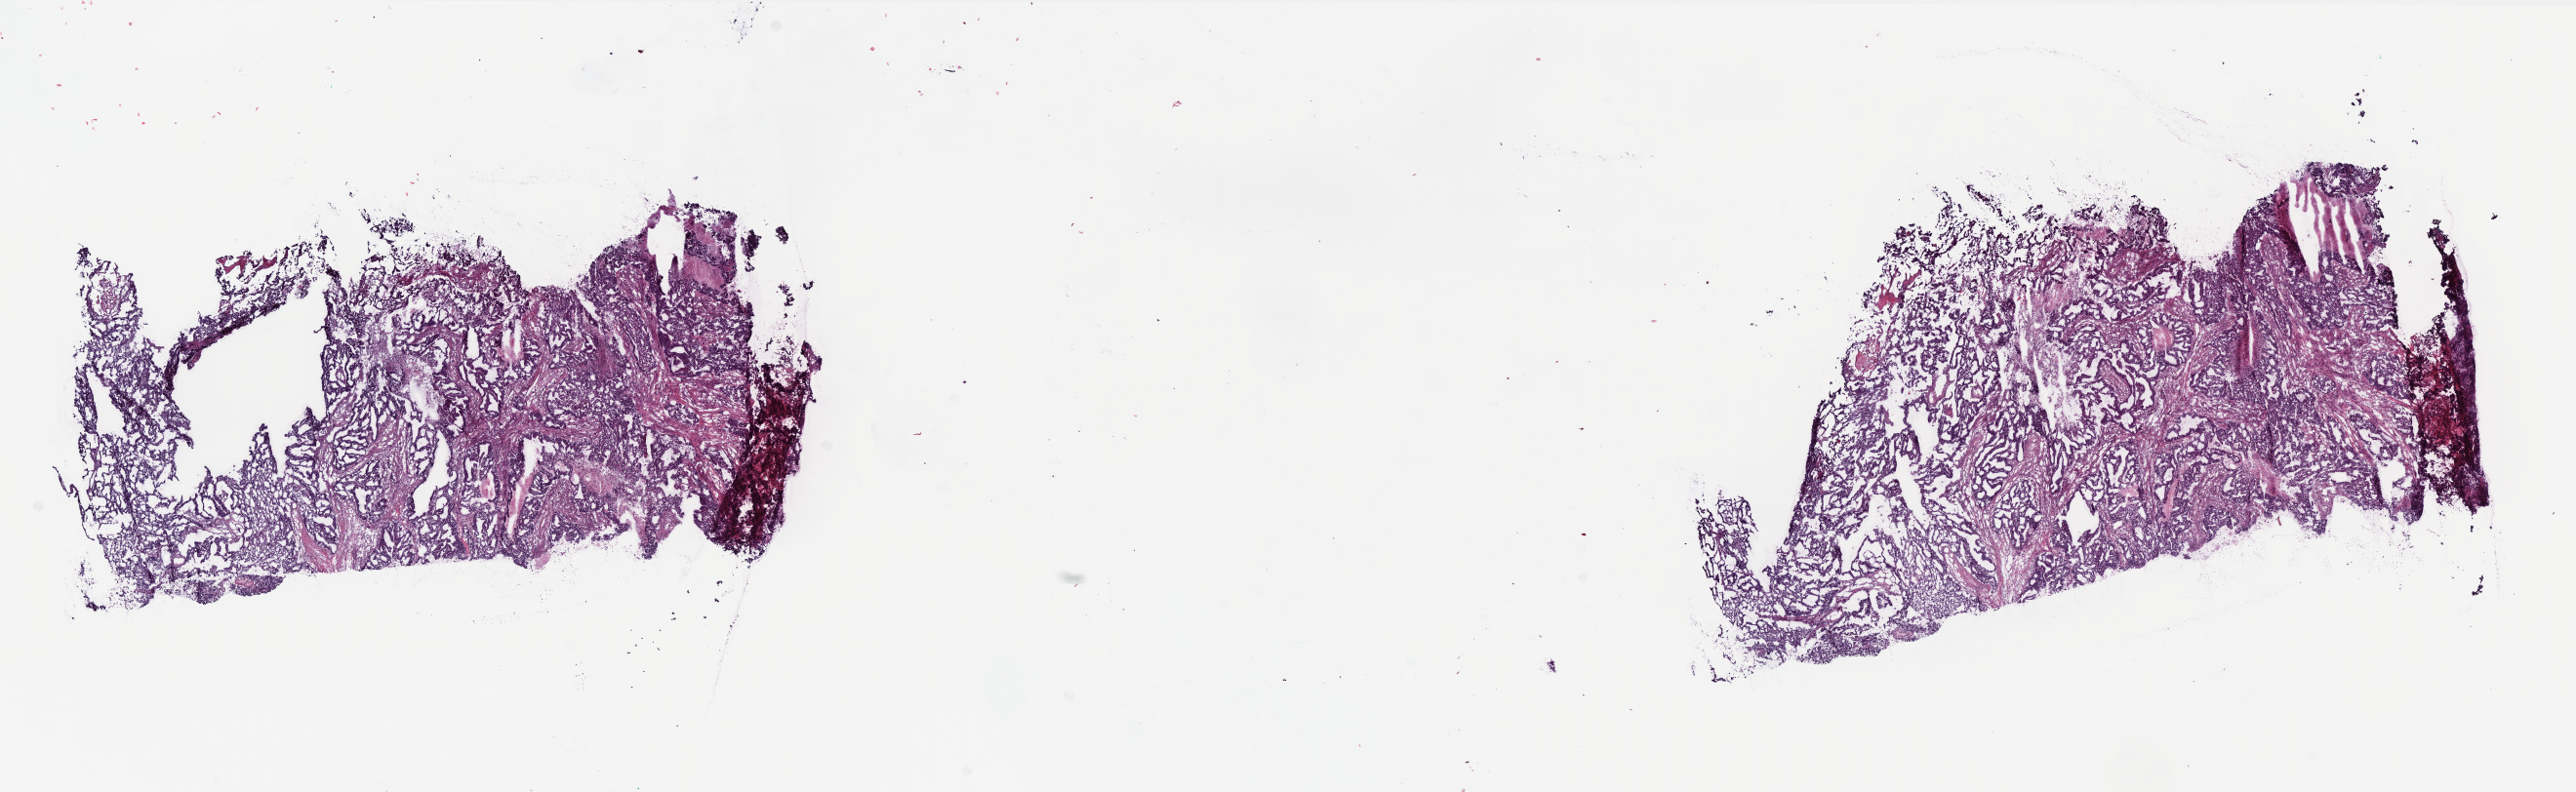
Whole-slide histology image, H&E — whole scanned area (about 21.2 x 6.5 mm) shown as a low-resolution overview. Frozen section from the top of the tissue portion. Primary tumour sample from the uterus. Patient: female, age at initial diagnosis 58 years. Histologic grade: G1 (well differentiated). Slide review estimates, as recorded: tumour cells 65%, tumour nuclei 65%, normal cells 0%, stromal cells 30%, necrosis 5%. Infiltration values recorded for this section: lymphocyte infiltration 15%, monocyte infiltration 10%, neutrophil infiltration 20%.
Histologic diagnosis: Endometrioid adenocarcinoma, NOS (endometrium). FIGO stage: IA.